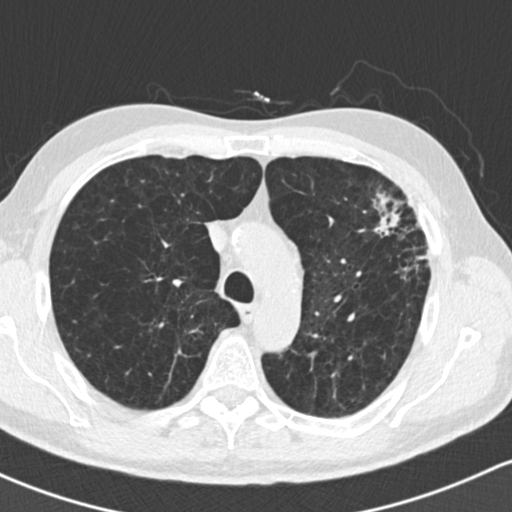
Low-dose screening chest CT, one axial slice; position 114 of 162 along the scan axis; reconstruction kernel B30f; lung window (W 1500 / L -600 HU); 2 mm slice thickness; 512 × 512 image matrix, field of view 318 × 318 mm.
Annotated regions visible in this slice (outlined manually by an expert reader):
- lesion 1 (tumor, upper lobe of left lung): box from (x=373, y=193) to (x=402, y=236) px